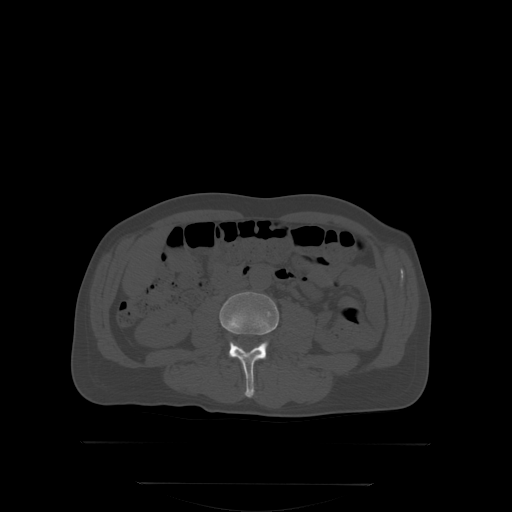
CT including the spine, one axial slice. Position 120 of 350 along the scan axis. Bone window (W 1800 / L 400 HU). 2.5 mm slice thickness. 512 × 512 image matrix, field of view 500 × 500 mm. Male patient, age 58 years. From the clinical record (not read from this slice): primary cancer: prostate; vertebrae with lytic lesions (as recorded): L1.
Outlined on this slice (semi-automatic segmentation, software-assisted and operator-edited):
- L3 vertebra: bounding box [x1, y1, x2, y2] px = [219, 292, 279, 396]